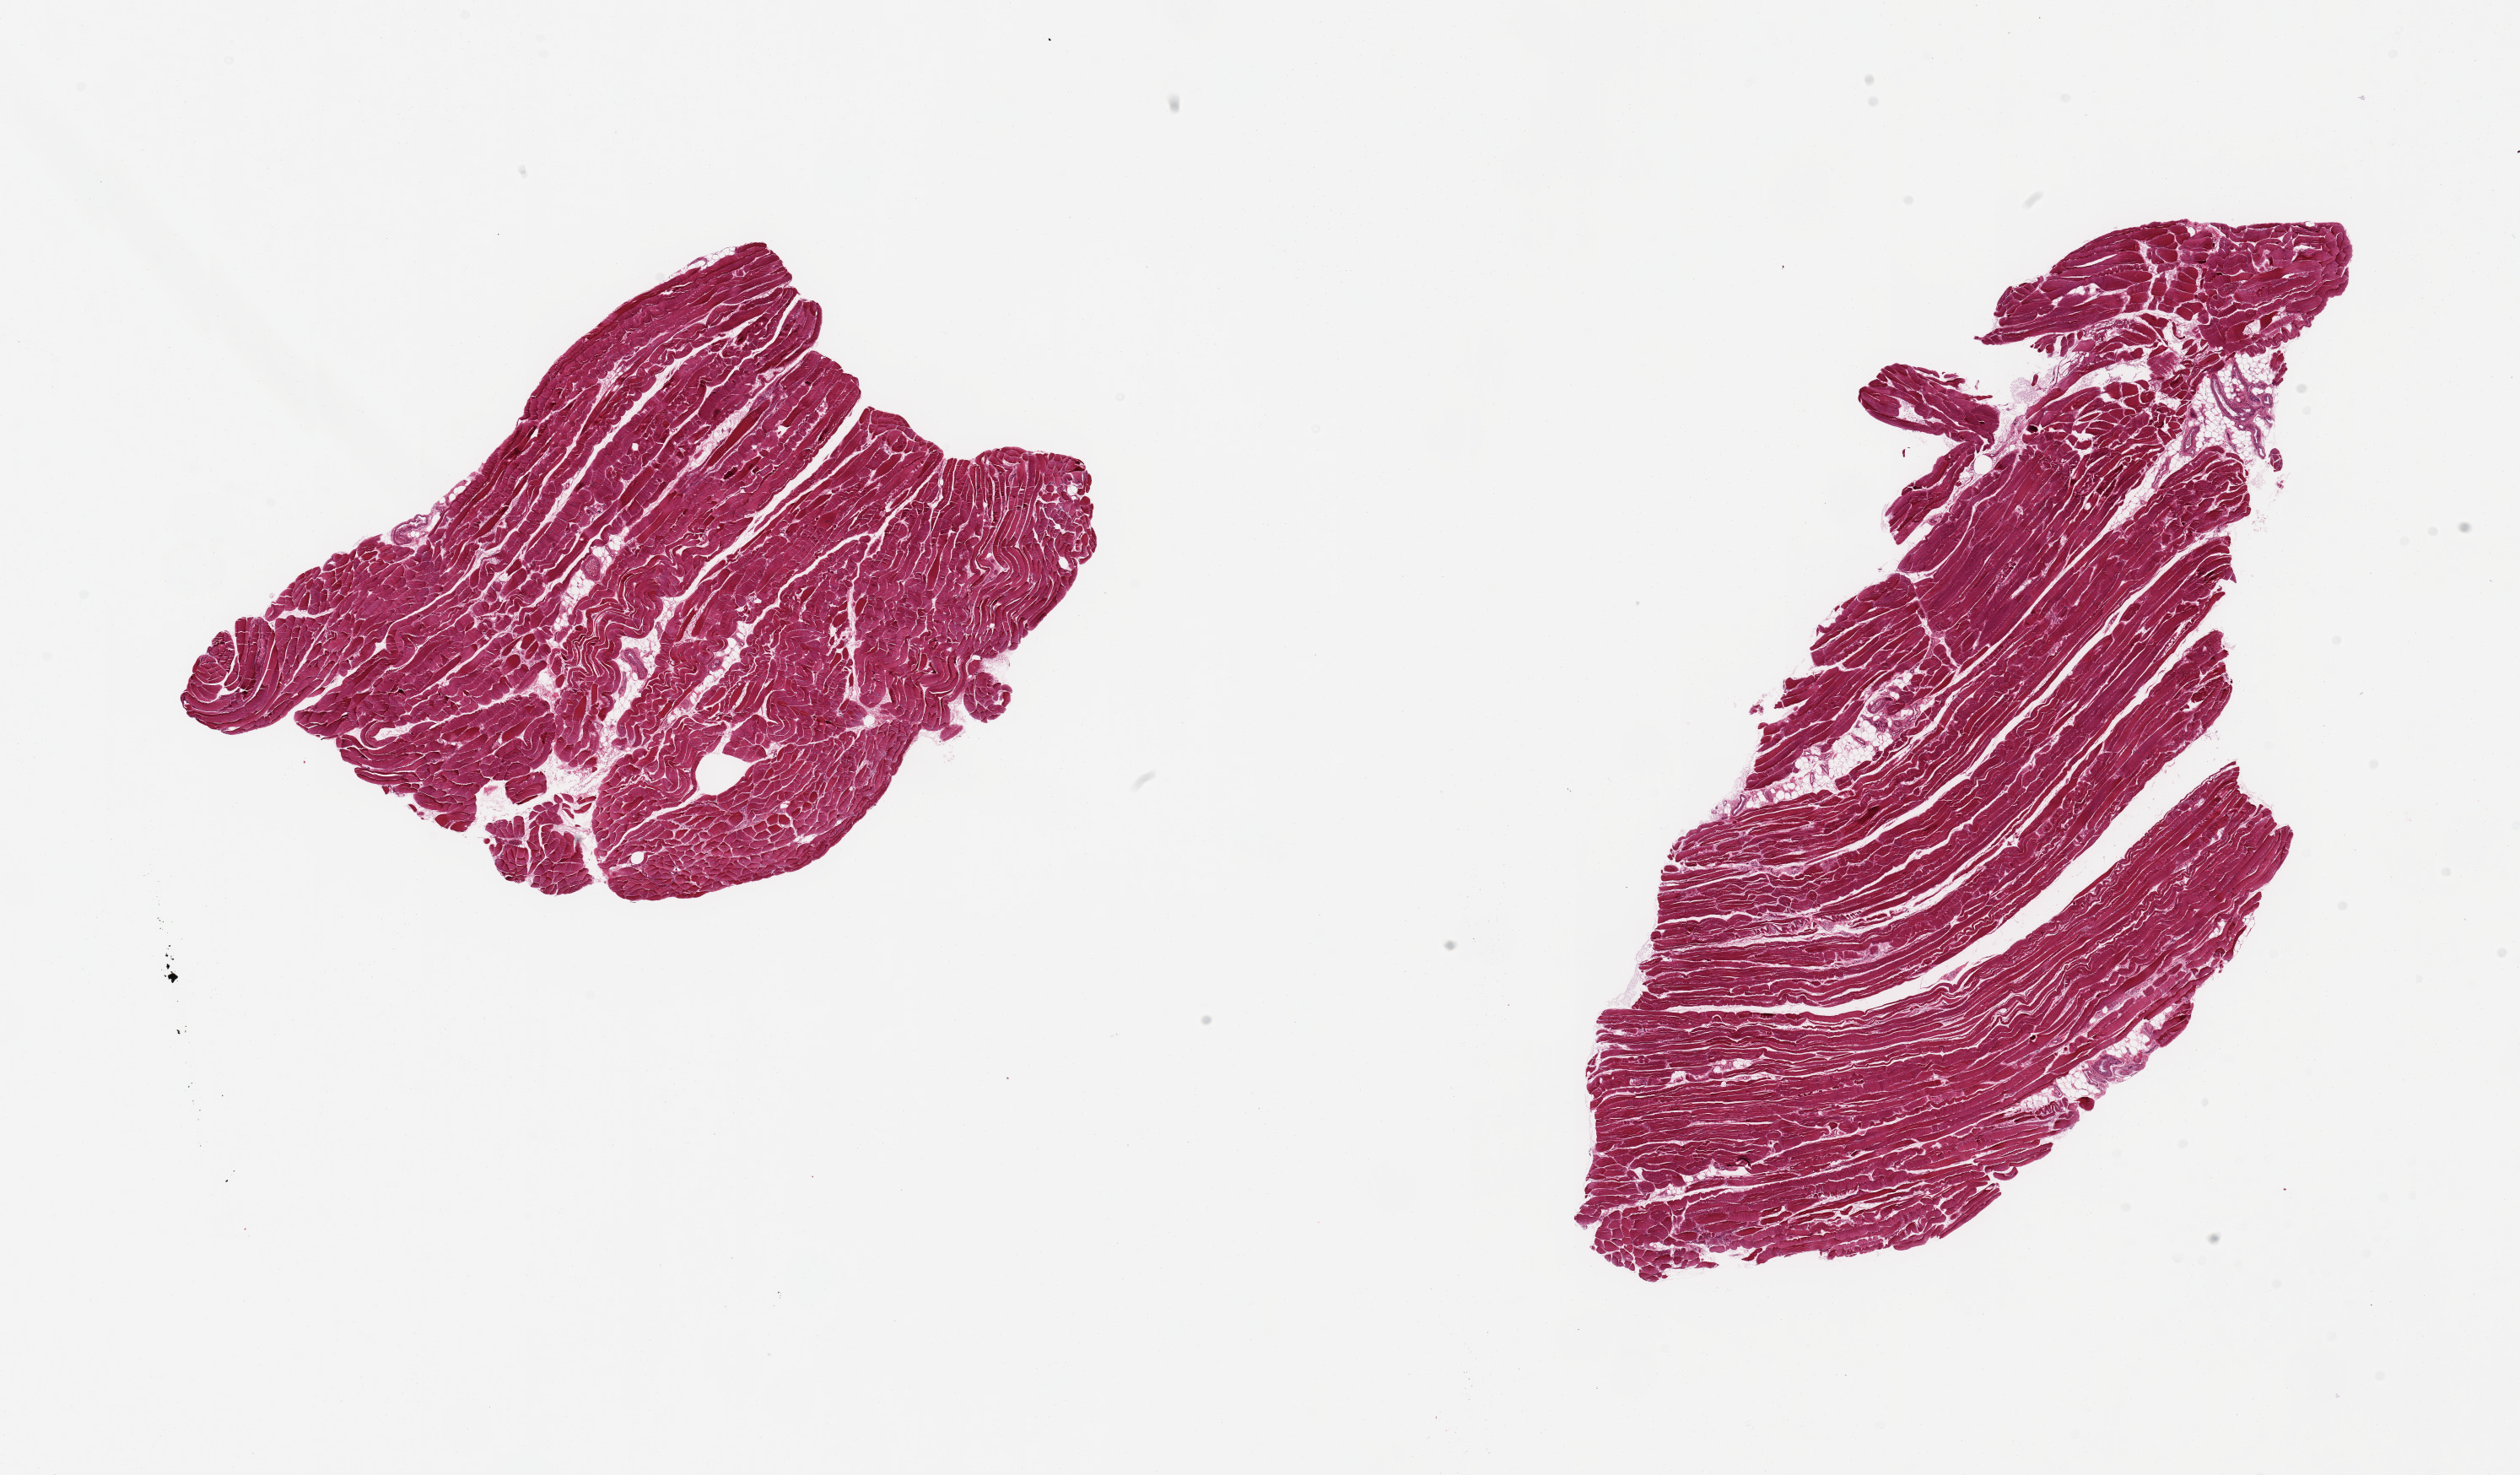
Whole-slide image, haematoxylin and eosin stain, brightfield — a low-resolution overview of the entire scanned area, about 23.6 x 13.8 mm. PAXgene-fixed, paraffin-embedded tissue. Section of skeletal muscle (target tissue). Tissue donor sample. Male donor.
Pathologist's review note for this sample: 2 pieces; up to 5-10% internal fat, rare atrophic fibers.